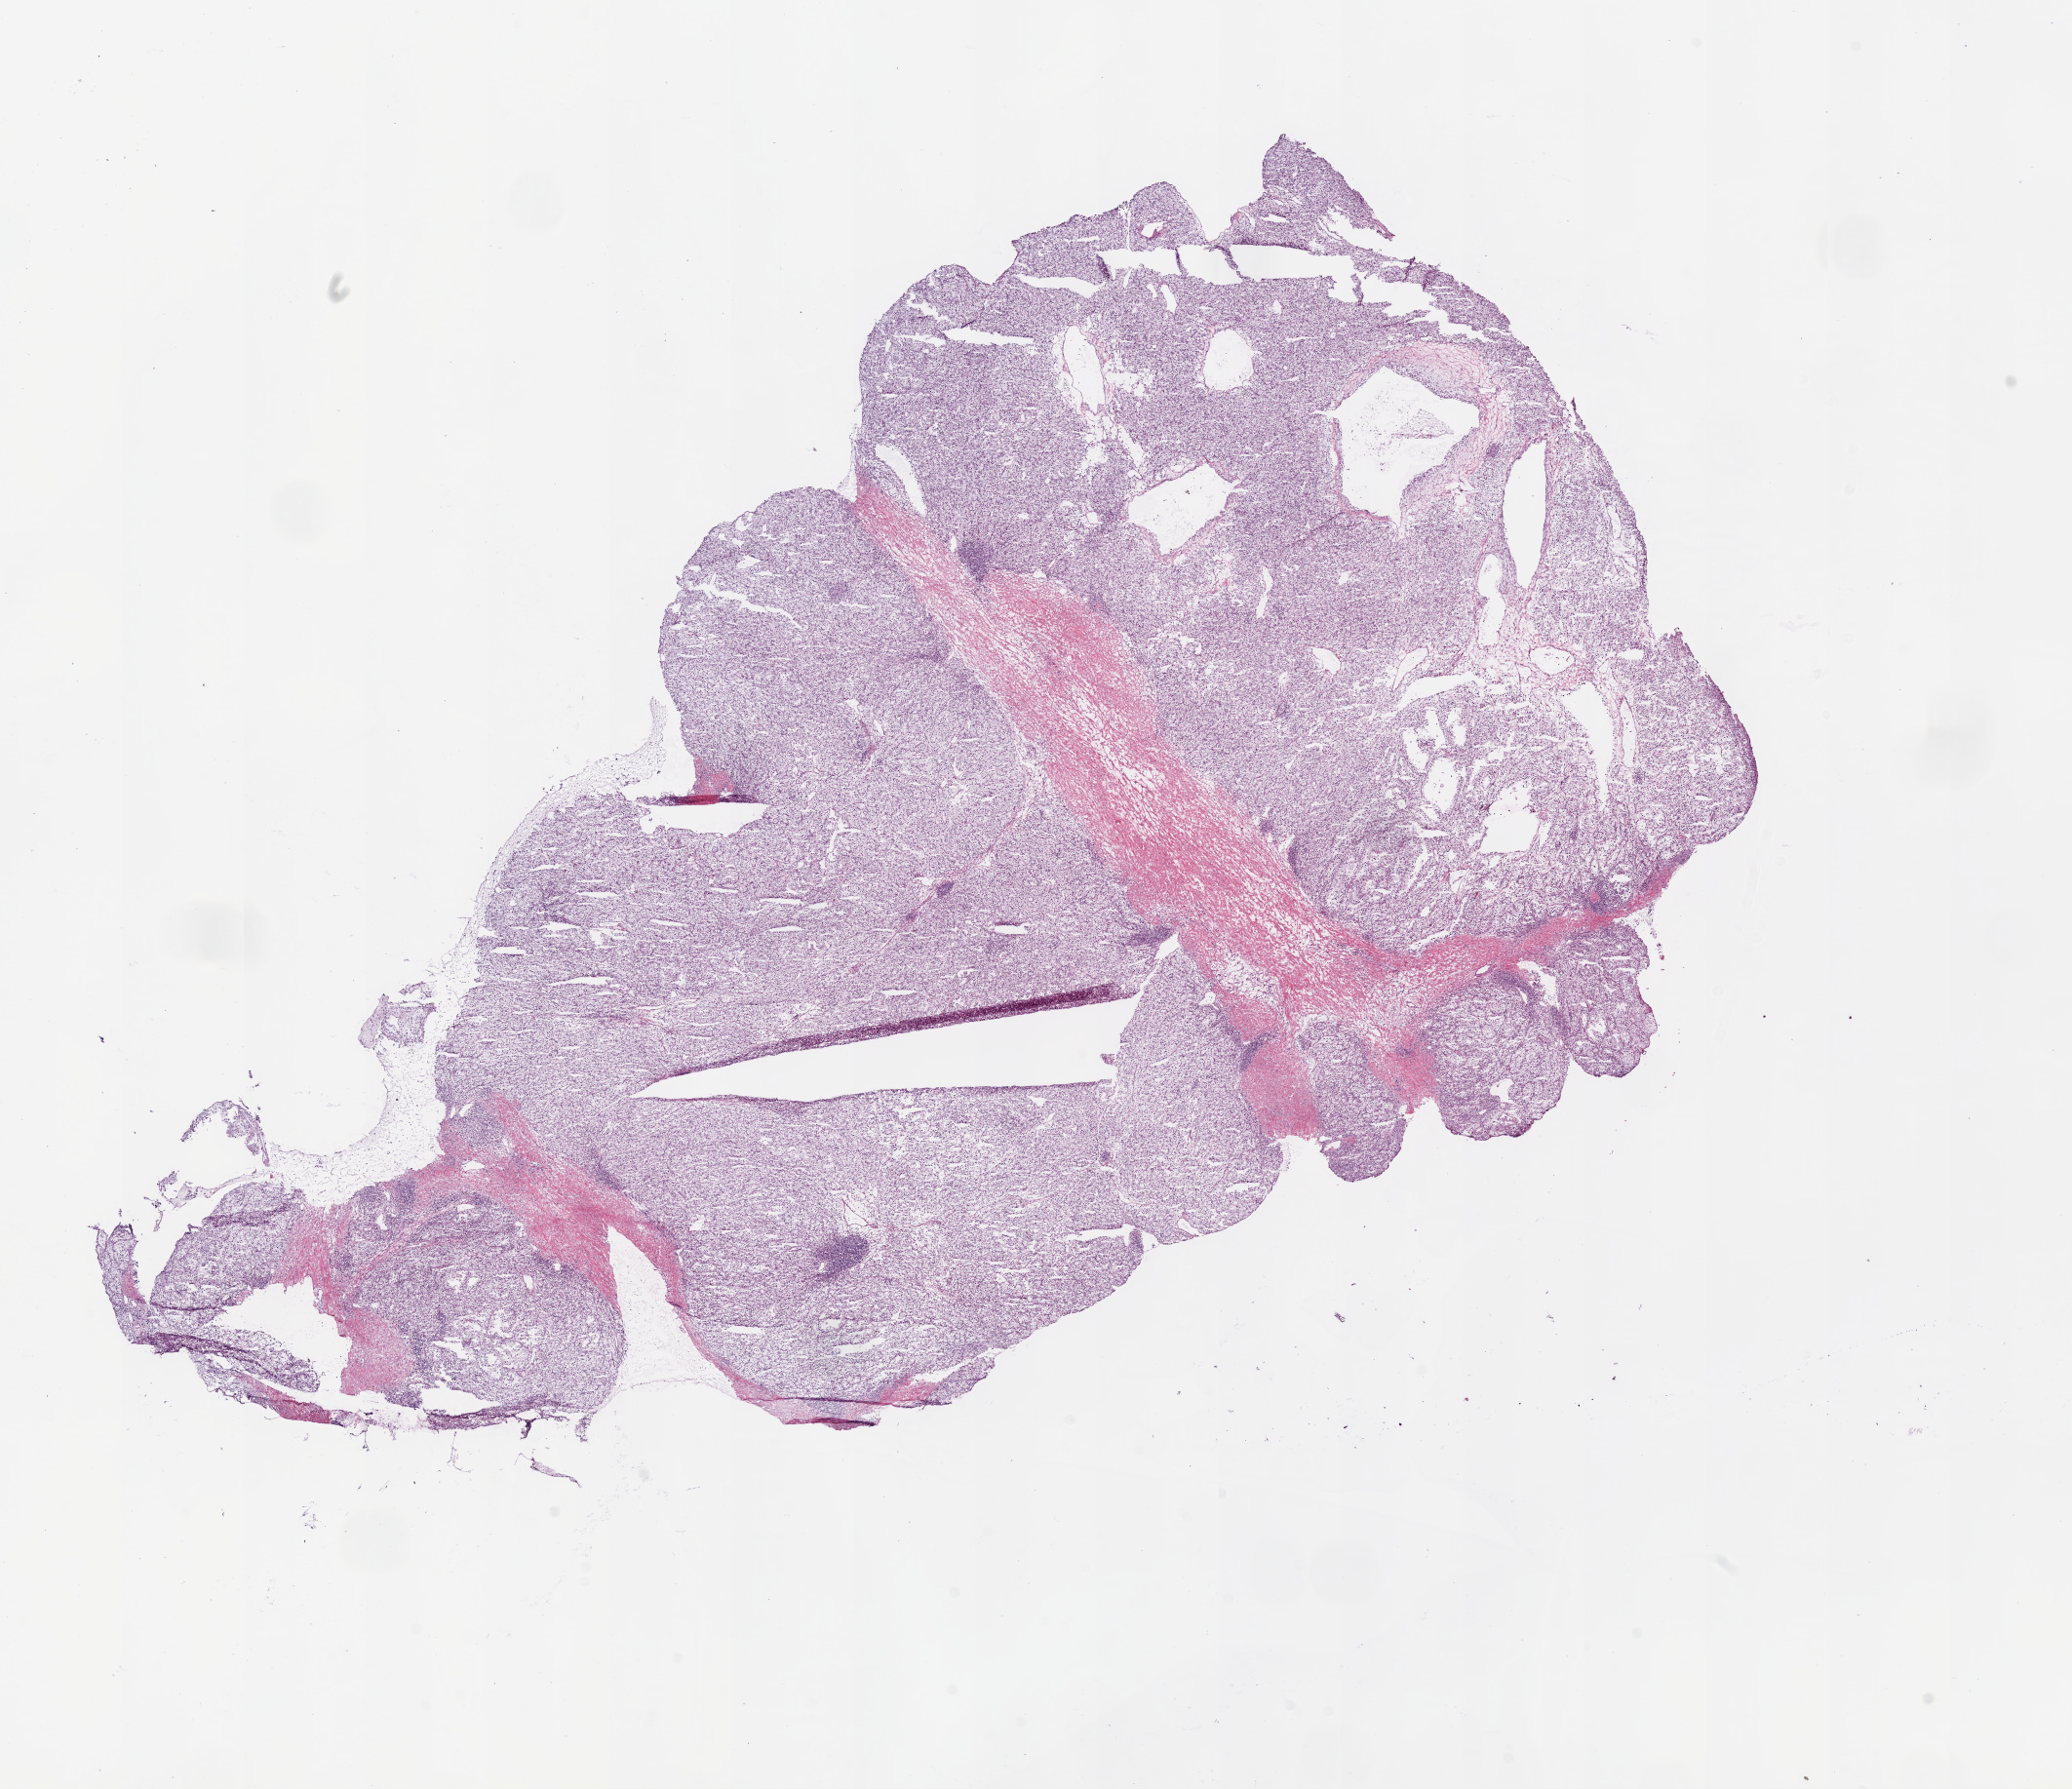
H&E whole-slide image, shown as a low-resolution overview of the whole scanned area (about 17.1 x 14.7 mm), frozen section from the bottom of the tissue portion, kidney, primary tumour sample. Female patient; age at initial diagnosis 60 years. Histologic grade: G2 (moderately differentiated). Slide review estimates, as recorded: tumour cells 90%, tumour nuclei 90%, normal cells 0%, stromal cells 10%, necrosis 0%.
Pathologic diagnosis: Clear cell adenocarcinoma, NOS. Laterality: left. AJCC pathologic stage: III.